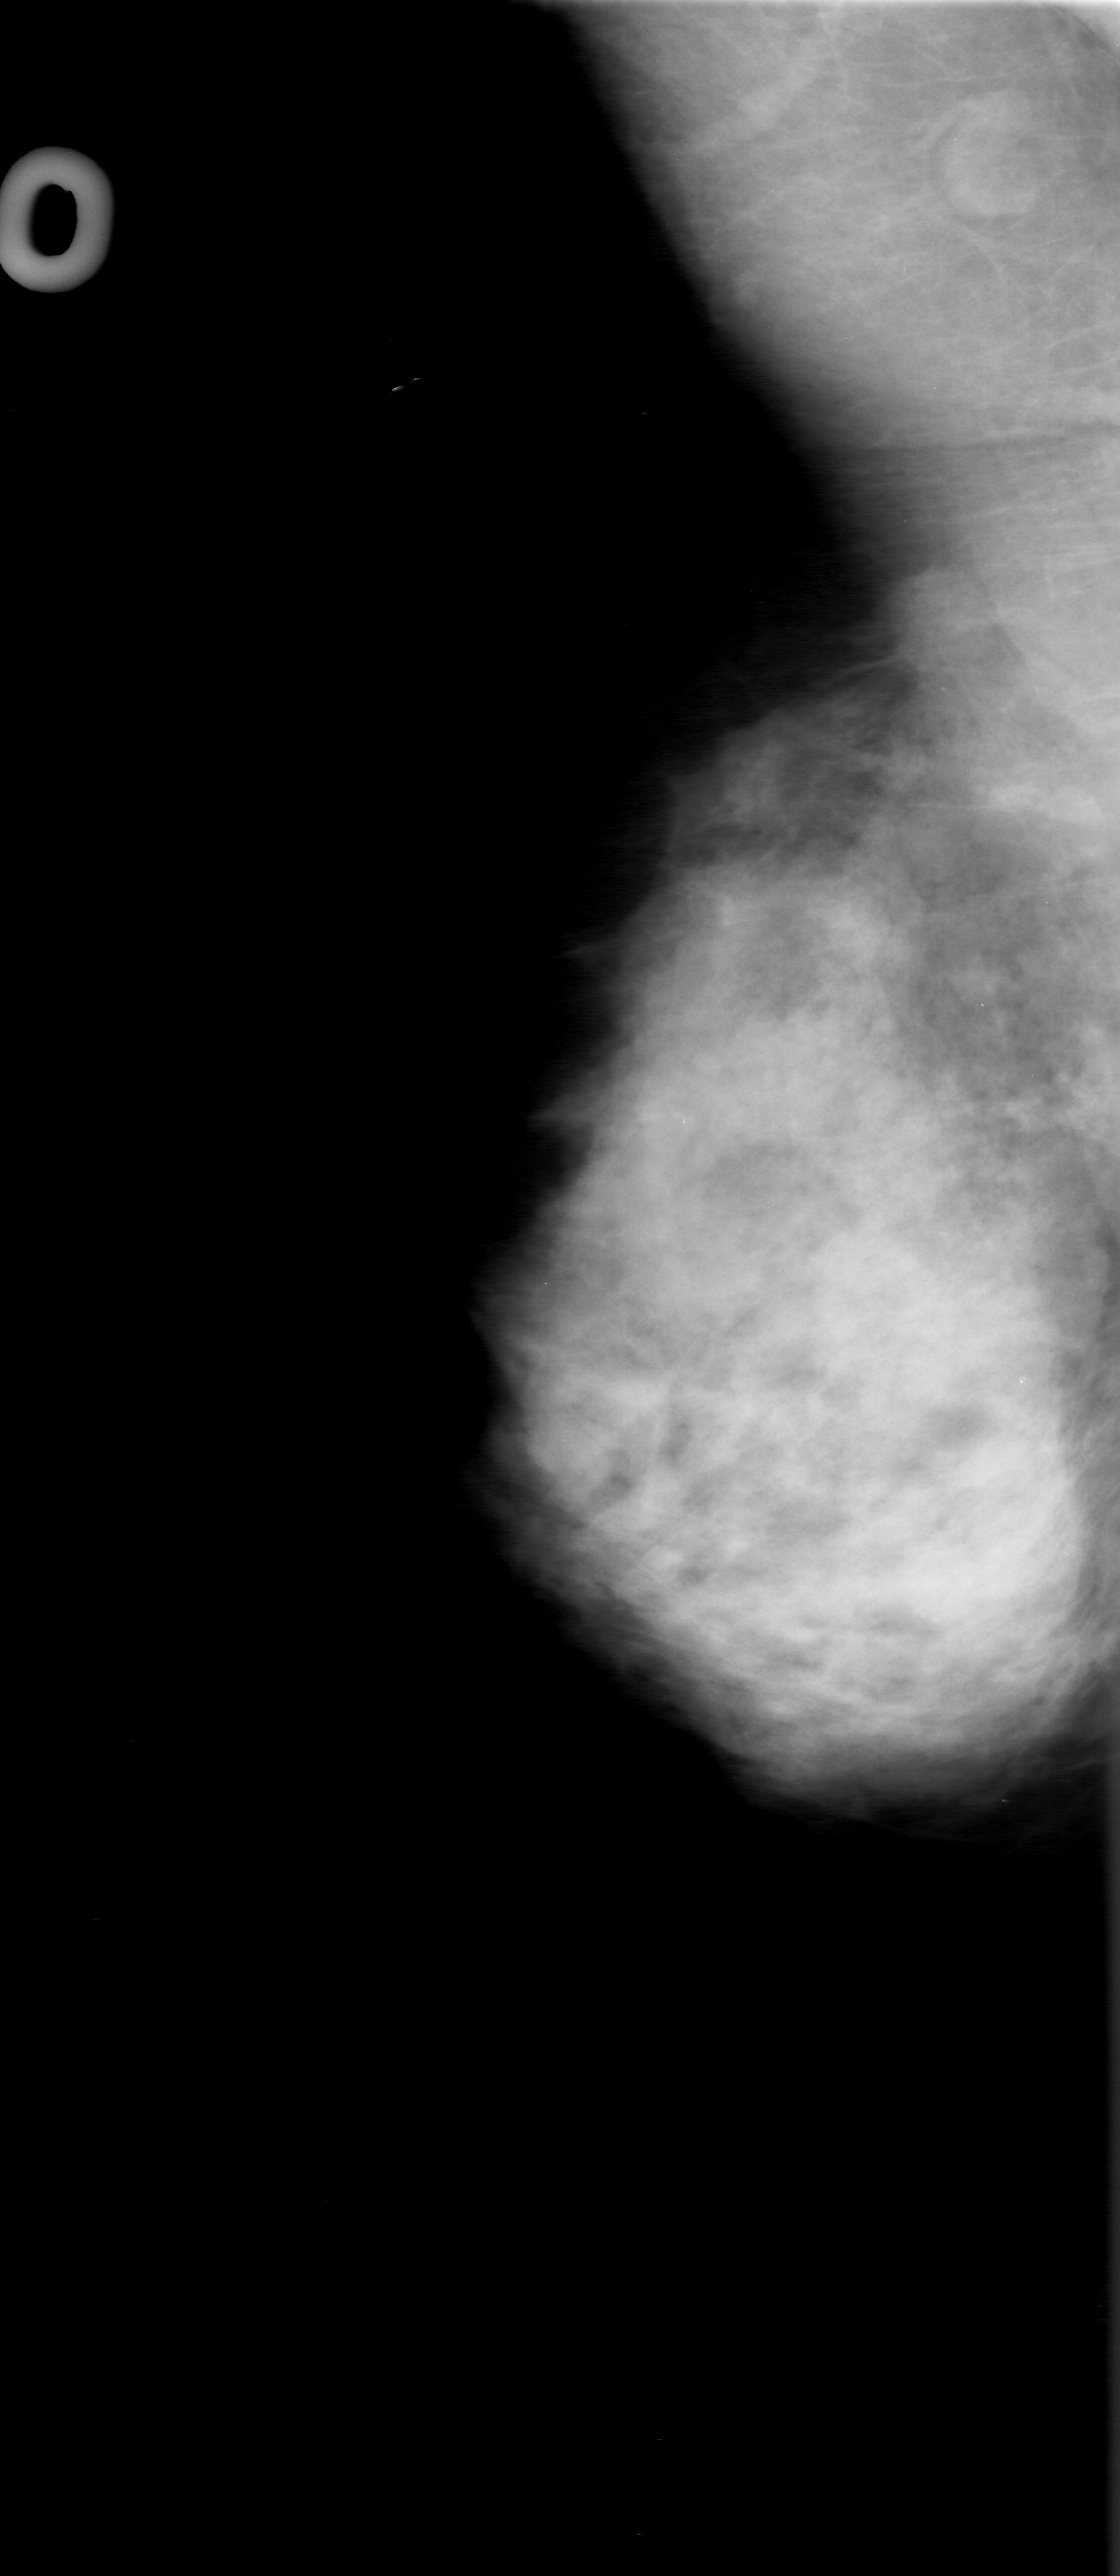
Scanned film-screen mammogram; right breast; MLO view; BI-RADS breast density category 4 (scale 1–4); 1120 × 2576 image matrix.
Marked abnormalities (boxes around the expert regions of interest):
- mass, shape round, margins spiculated; BI-RADS assessment category 3; subtlety rating 3 on a 1 (subtle) to 5 (obvious) scale; pathology (as recorded): malignant: bounding box (x1, y1, x2, y2) in pixels: (854, 560, 1050, 782)